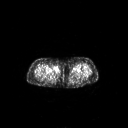
FDG PET of an extremity soft-tissue mass (from a PET/CT study), one axial slice. Slice 239 of 311 in the series (ordered by position). 3.27 mm slice thickness. 128 × 128 image matrix, field of view 700 × 700 mm. Female patient, age 78 years. Case-level facts recorded for this patient, not image findings: histological type: leiomyosarcoma; grade: intermediate; site of the primary tumour: parascapusular.
Annotated regions visible in this slice (expert contour drawn on MRI and transferred to this co-registered scan by the dataset authors):
- gross tumour volume including surrounding oedema: box from (x=52, y=65) to (x=61, y=74) px
- gross tumour volume (mass): (x=52, y=65)–(x=59, y=74)